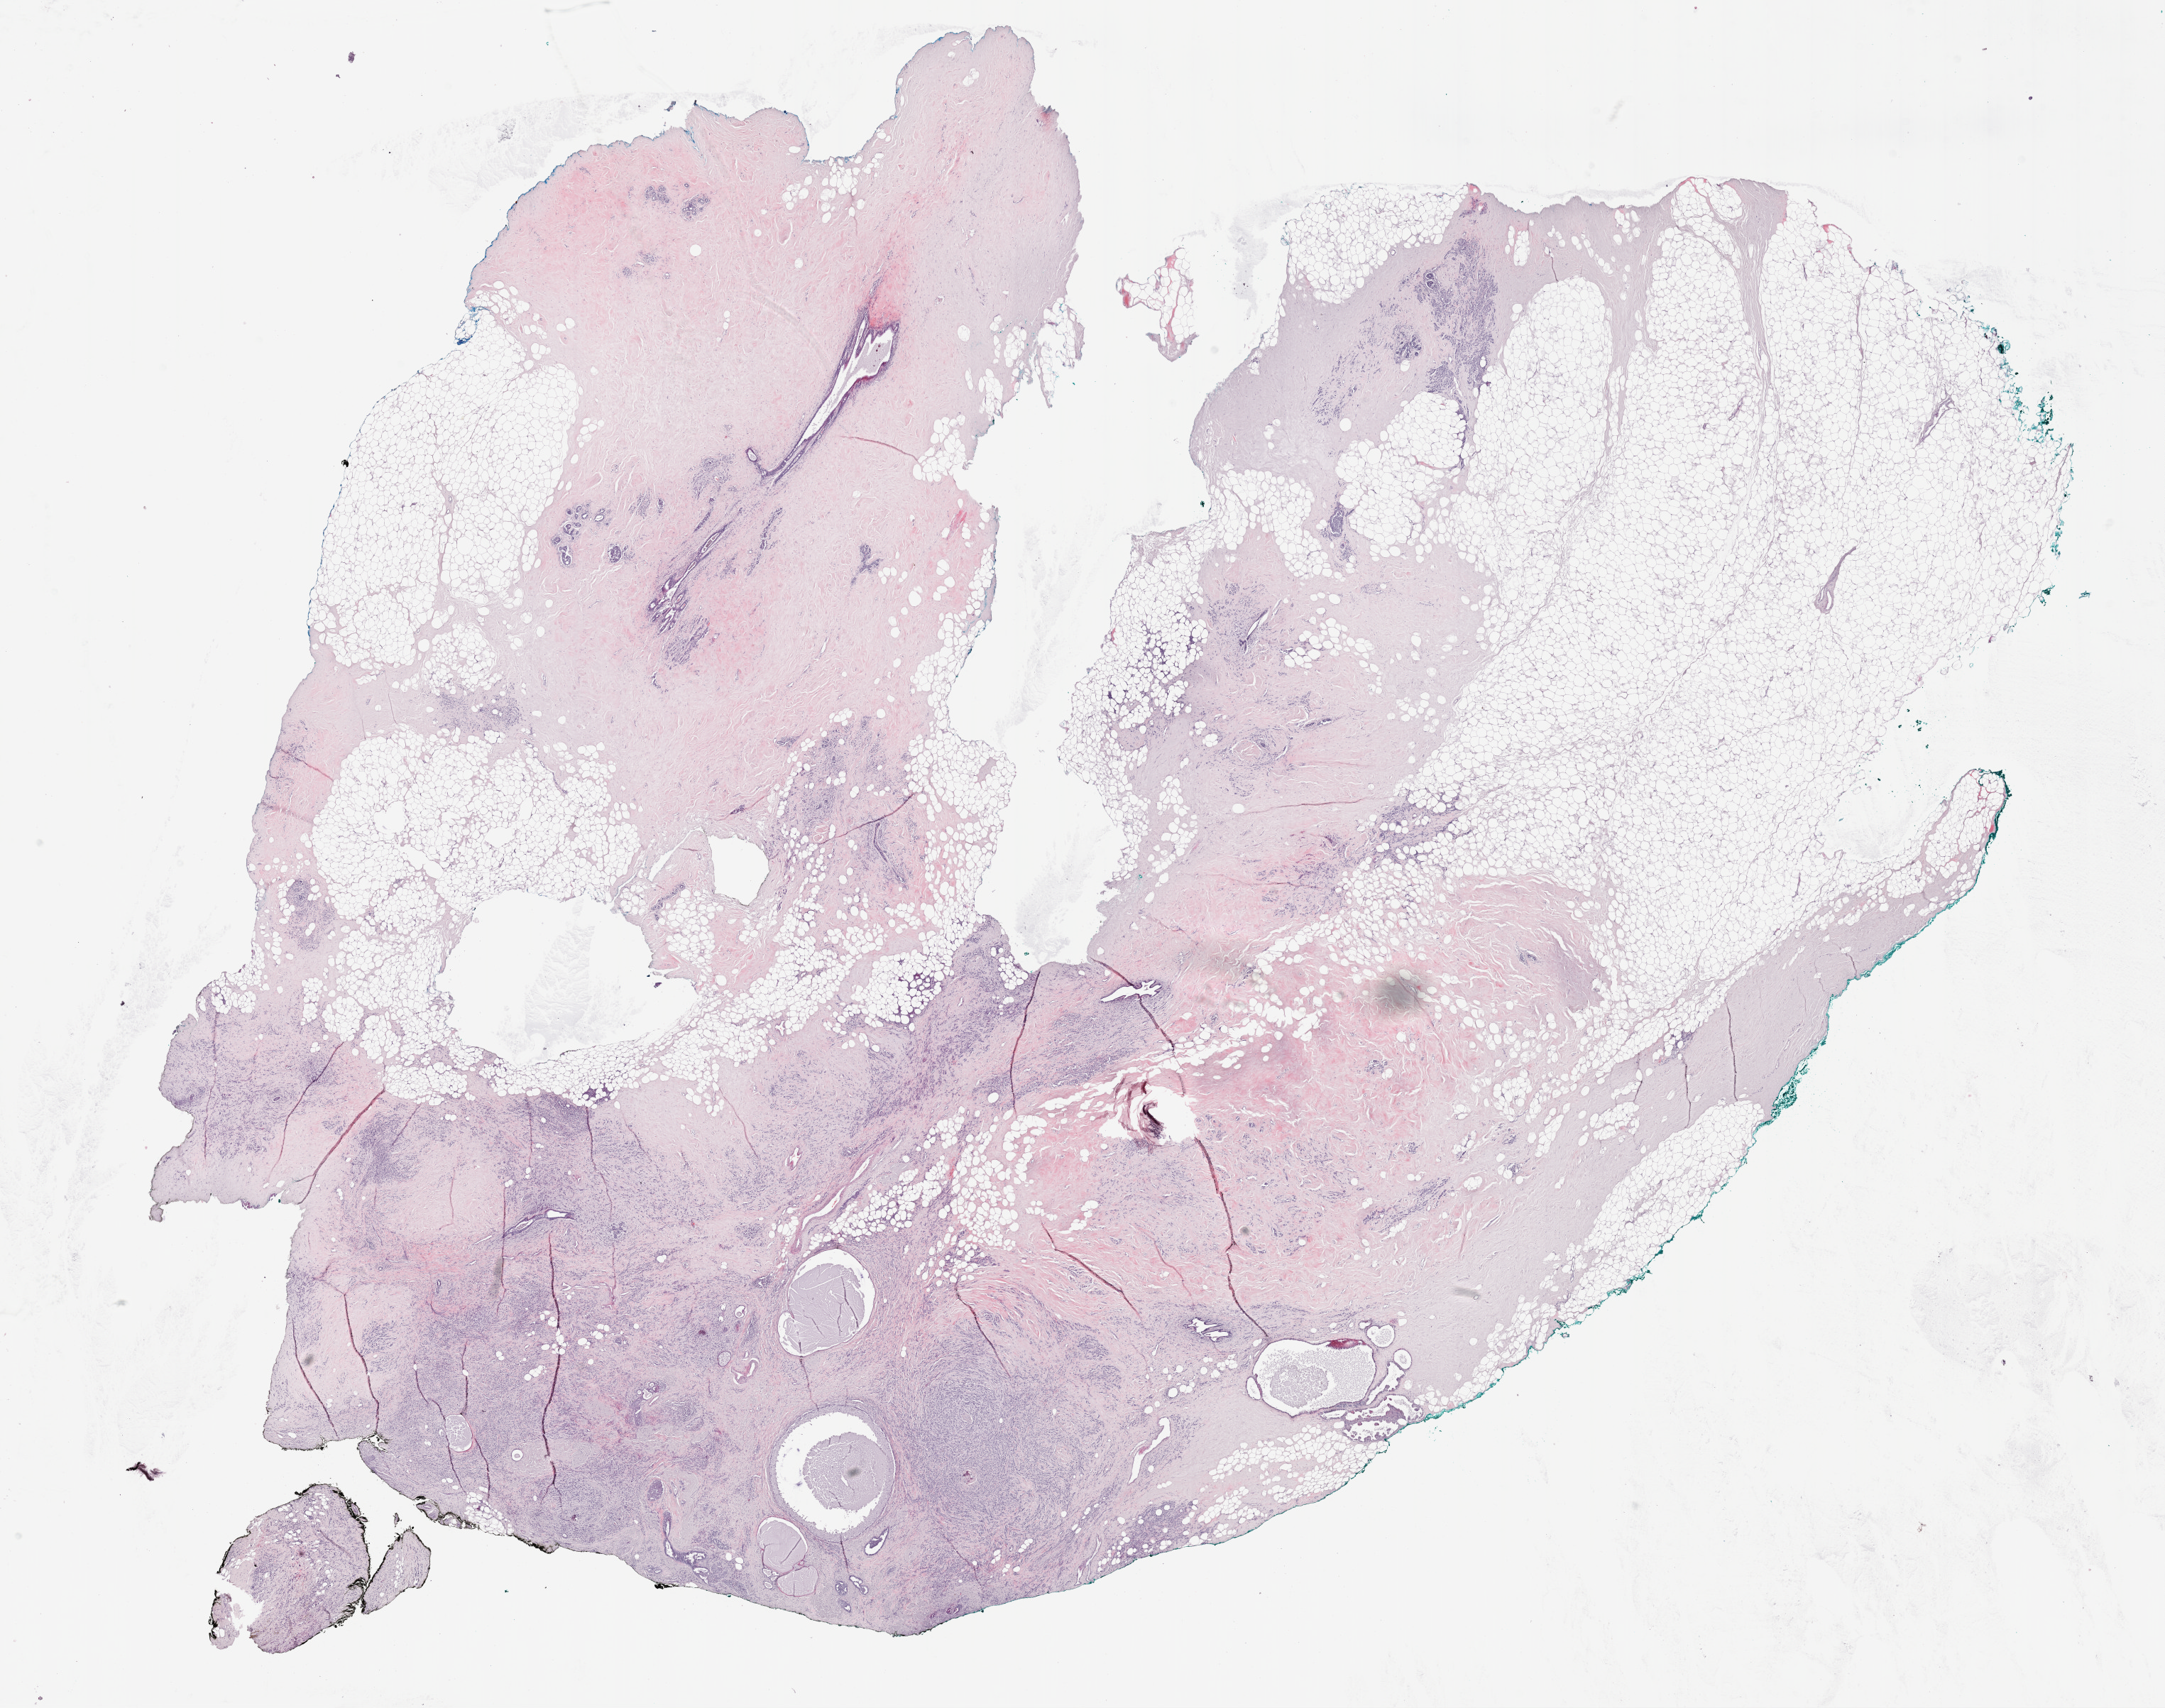
Hematoxylin and eosin (H&E) stained whole-slide image, a low-resolution overview of the entire scanned area, about 24.7 x 19.5 mm. Formalin-fixed paraffin-embedded (FFPE) diagnostic section. Sample: primary tumour, breast. Patient: female, age at initial diagnosis 60 years.
Laterality: left. Diagnosis: Lobular carcinoma, NOS. AJCC pathologic stage: IIIA.